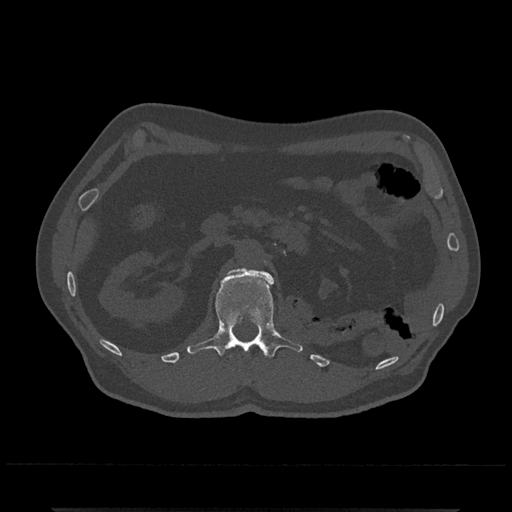
CT including the spine, one axial slice. Slice 363 of 797 in the series (ordered by position). Bone window (W 1800 / L 400 HU). 0.5 mm slice thickness. 512 × 512 image matrix. Patient: male, 67 years. From the clinical record (not read from this slice): primary cancer: prostate.
Outlined on this slice (semi-automatic segmentation, software-assisted and operator-edited):
- L1 vertebra: bounding box [x1, y1, x2, y2] px = [187, 267, 303, 357]